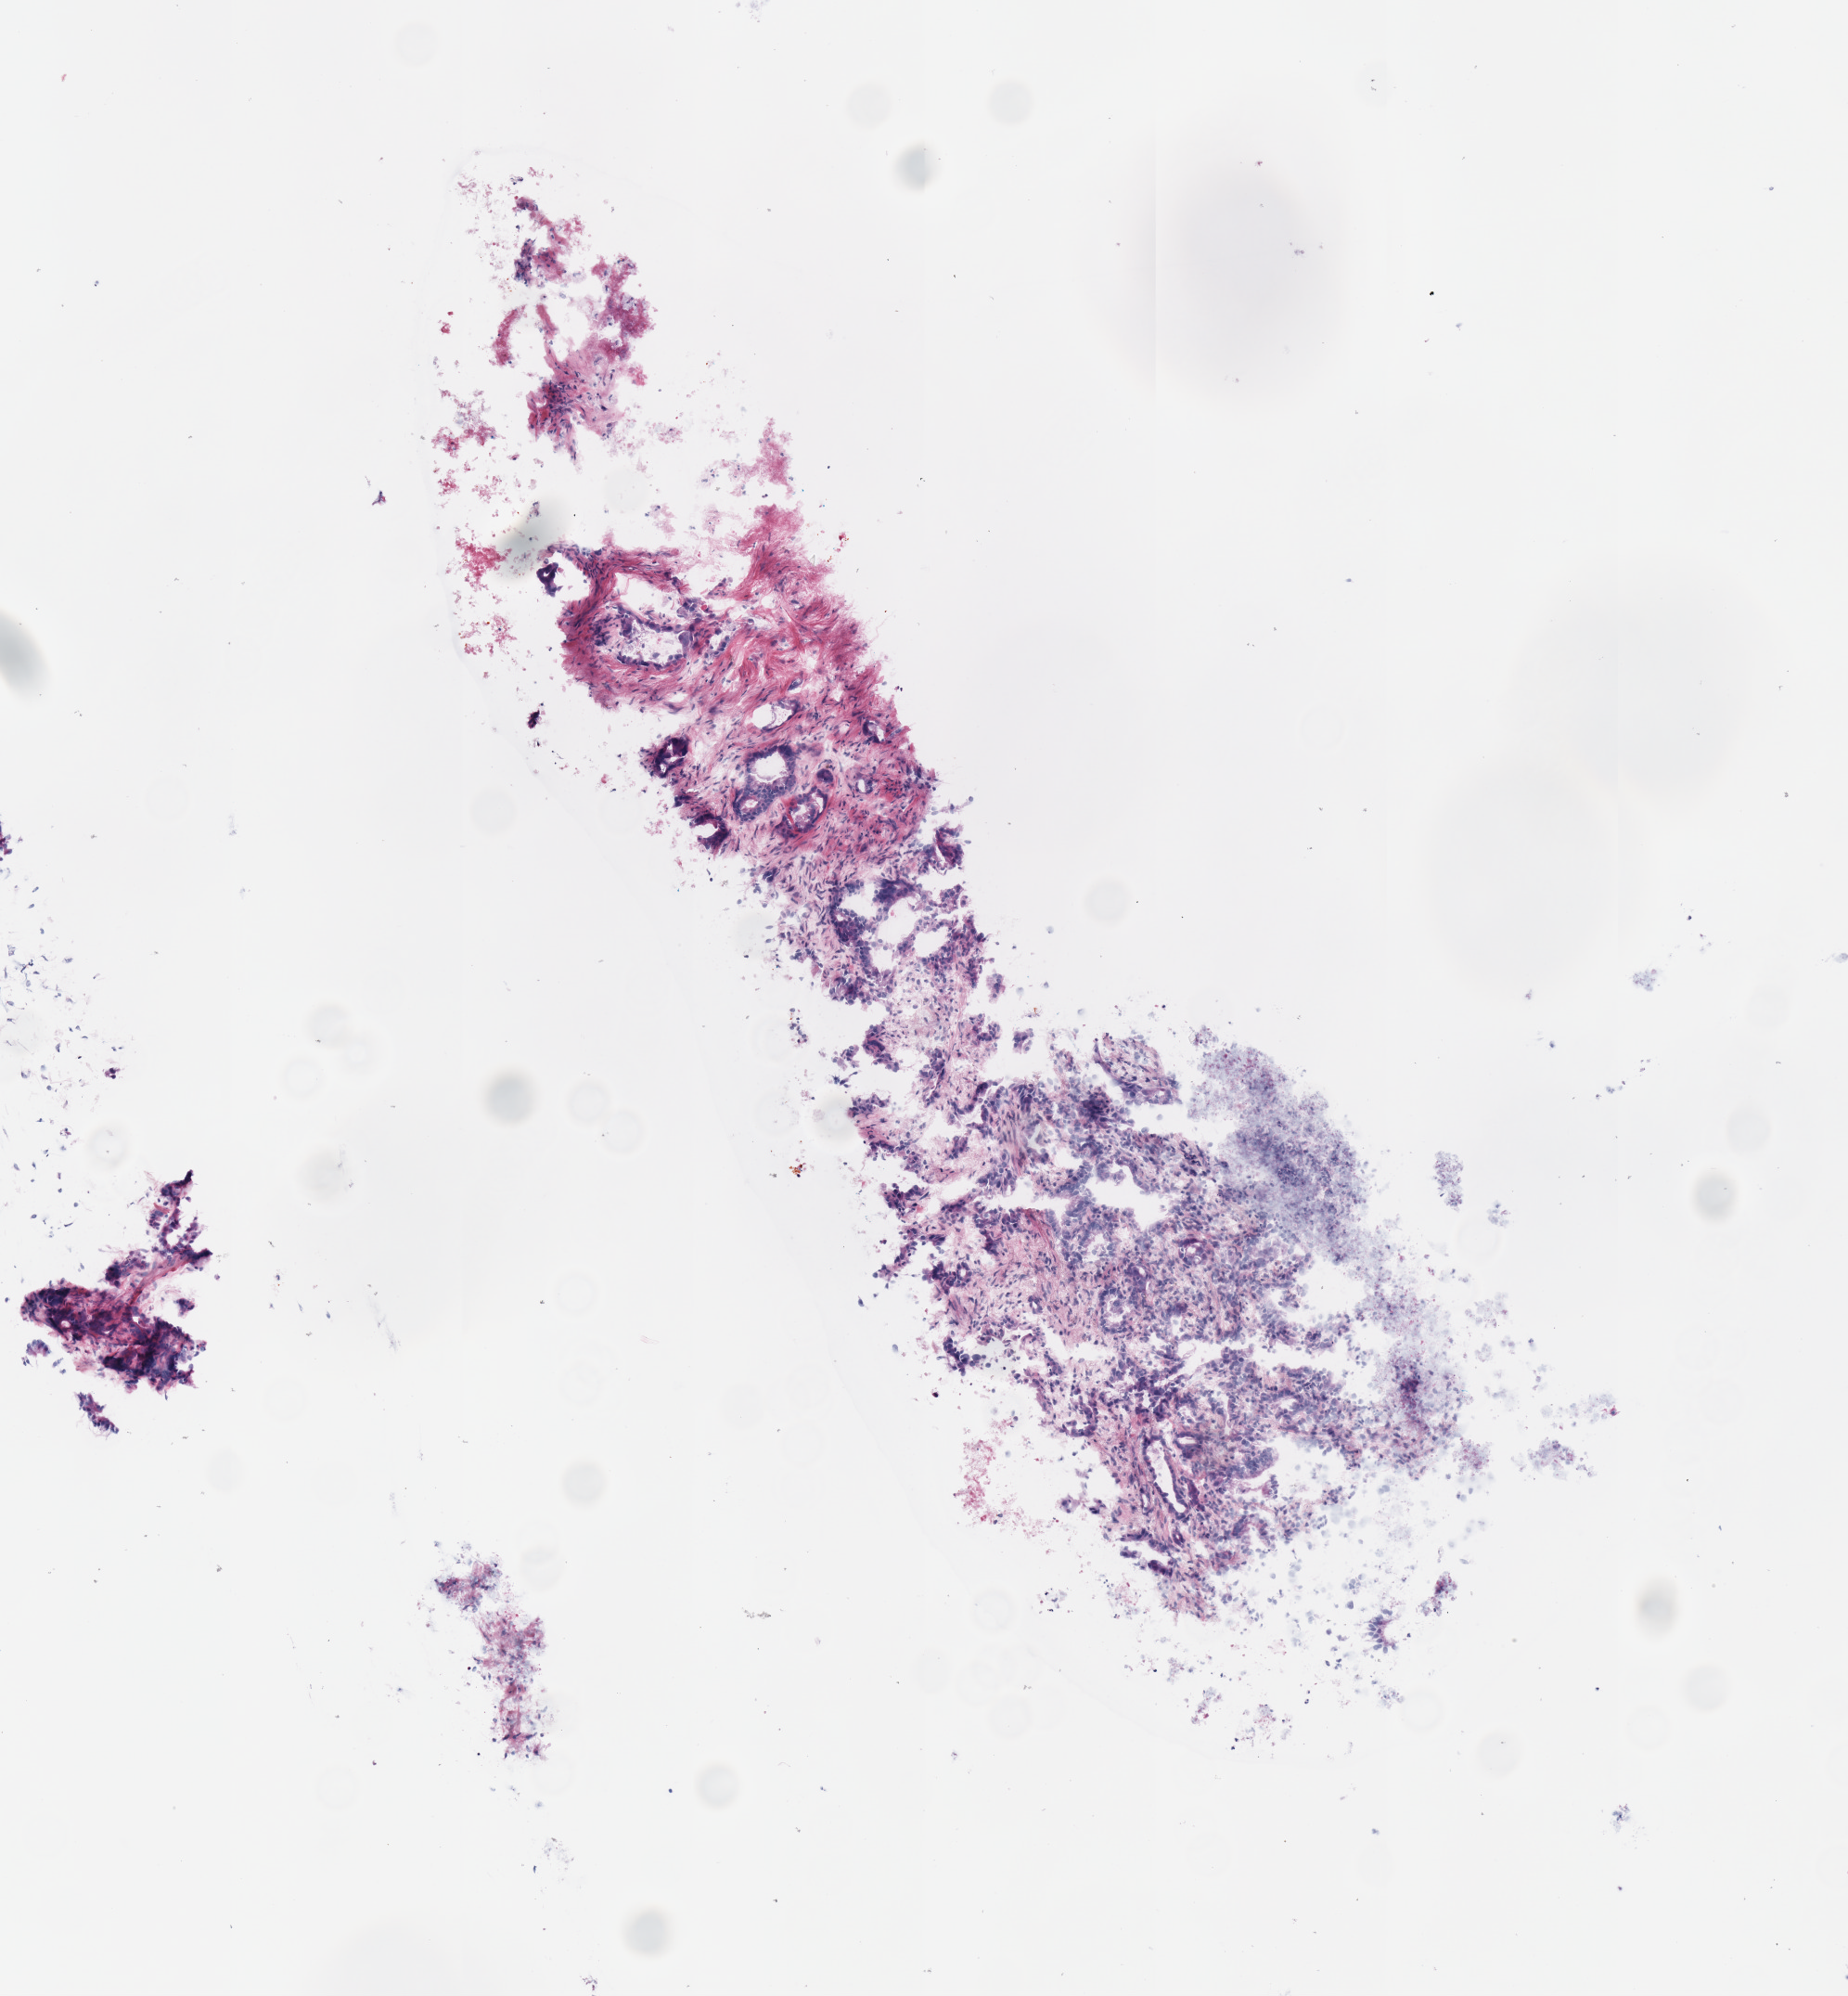
Digitized H&E-stained tissue section (whole slide), low-resolution overview of the scanned area, about 3.9 x 4.2 mm (slide scanned at 40x). Frozen section from the top of the tissue portion. Sample: primary tumour, pancreas. Female, age 62 years at initial diagnosis. Histologic grade: G2 (moderately differentiated). Pathologist review of this section (percent, as recorded): tumour cells 70%, tumour nuclei 75%, normal cells 0%, stromal cells 20%, necrosis 10%.
AJCC pathologic stage: IIB (7th edition). Diagnosis: Infiltrating duct carcinoma, NOS.